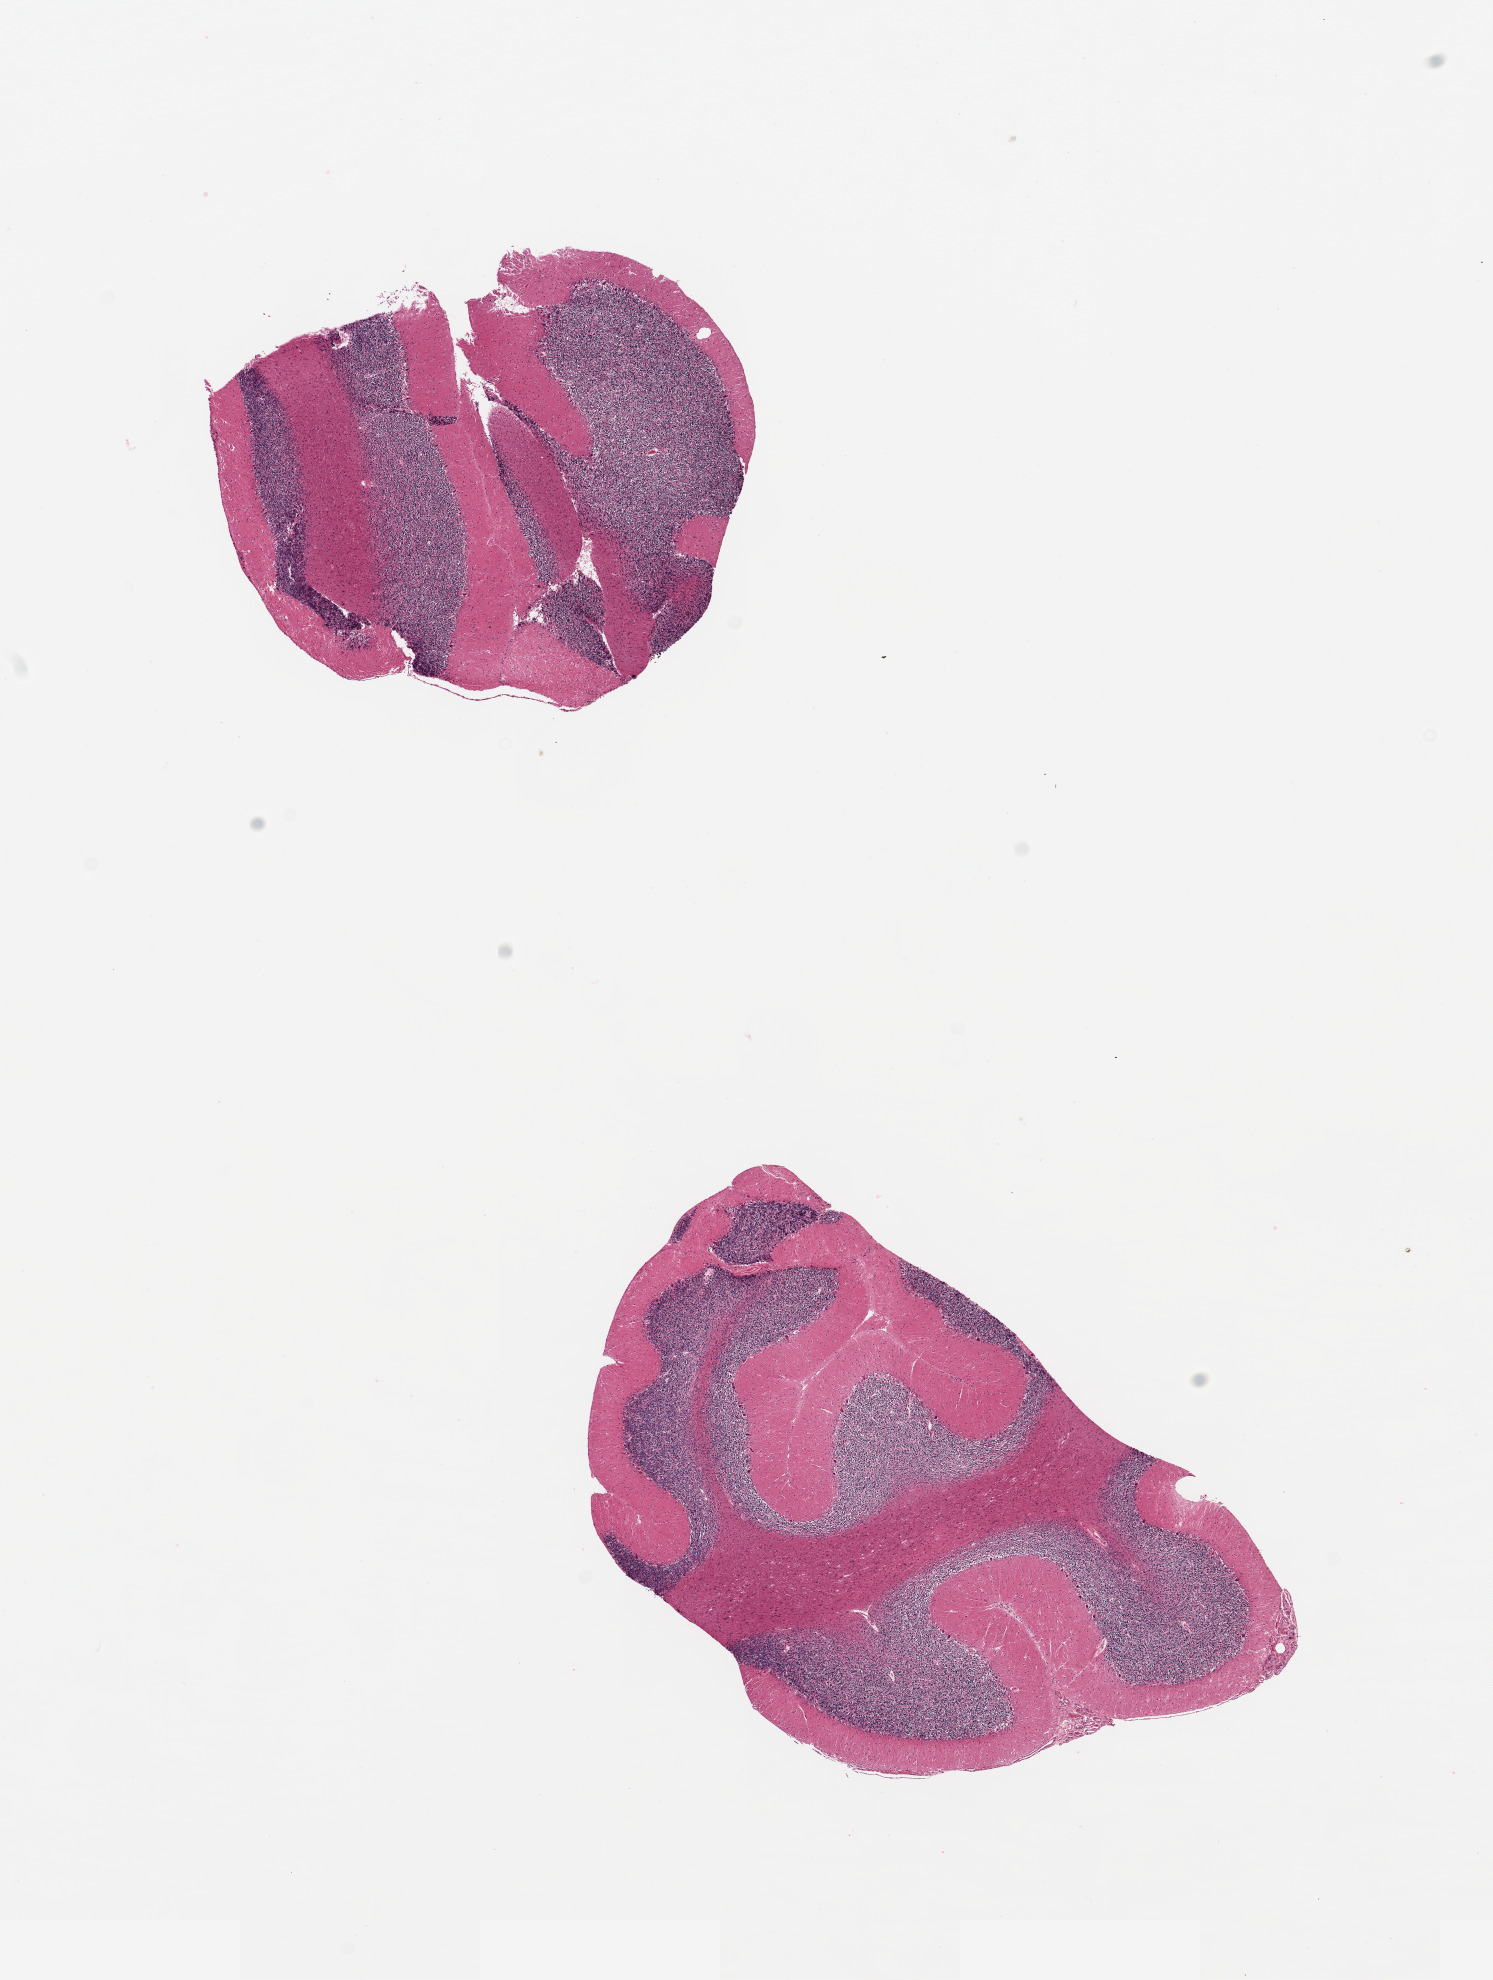
Whole-slide image, H&E stain — a low-resolution overview of the entire scanned area, about 11.8 x 15.7 mm. PAXgene-fixed, paraffin-embedded tissue. Section of cerebellum (target tissue). Tissue donor sample.
Review note (as recorded): 2 pieces.